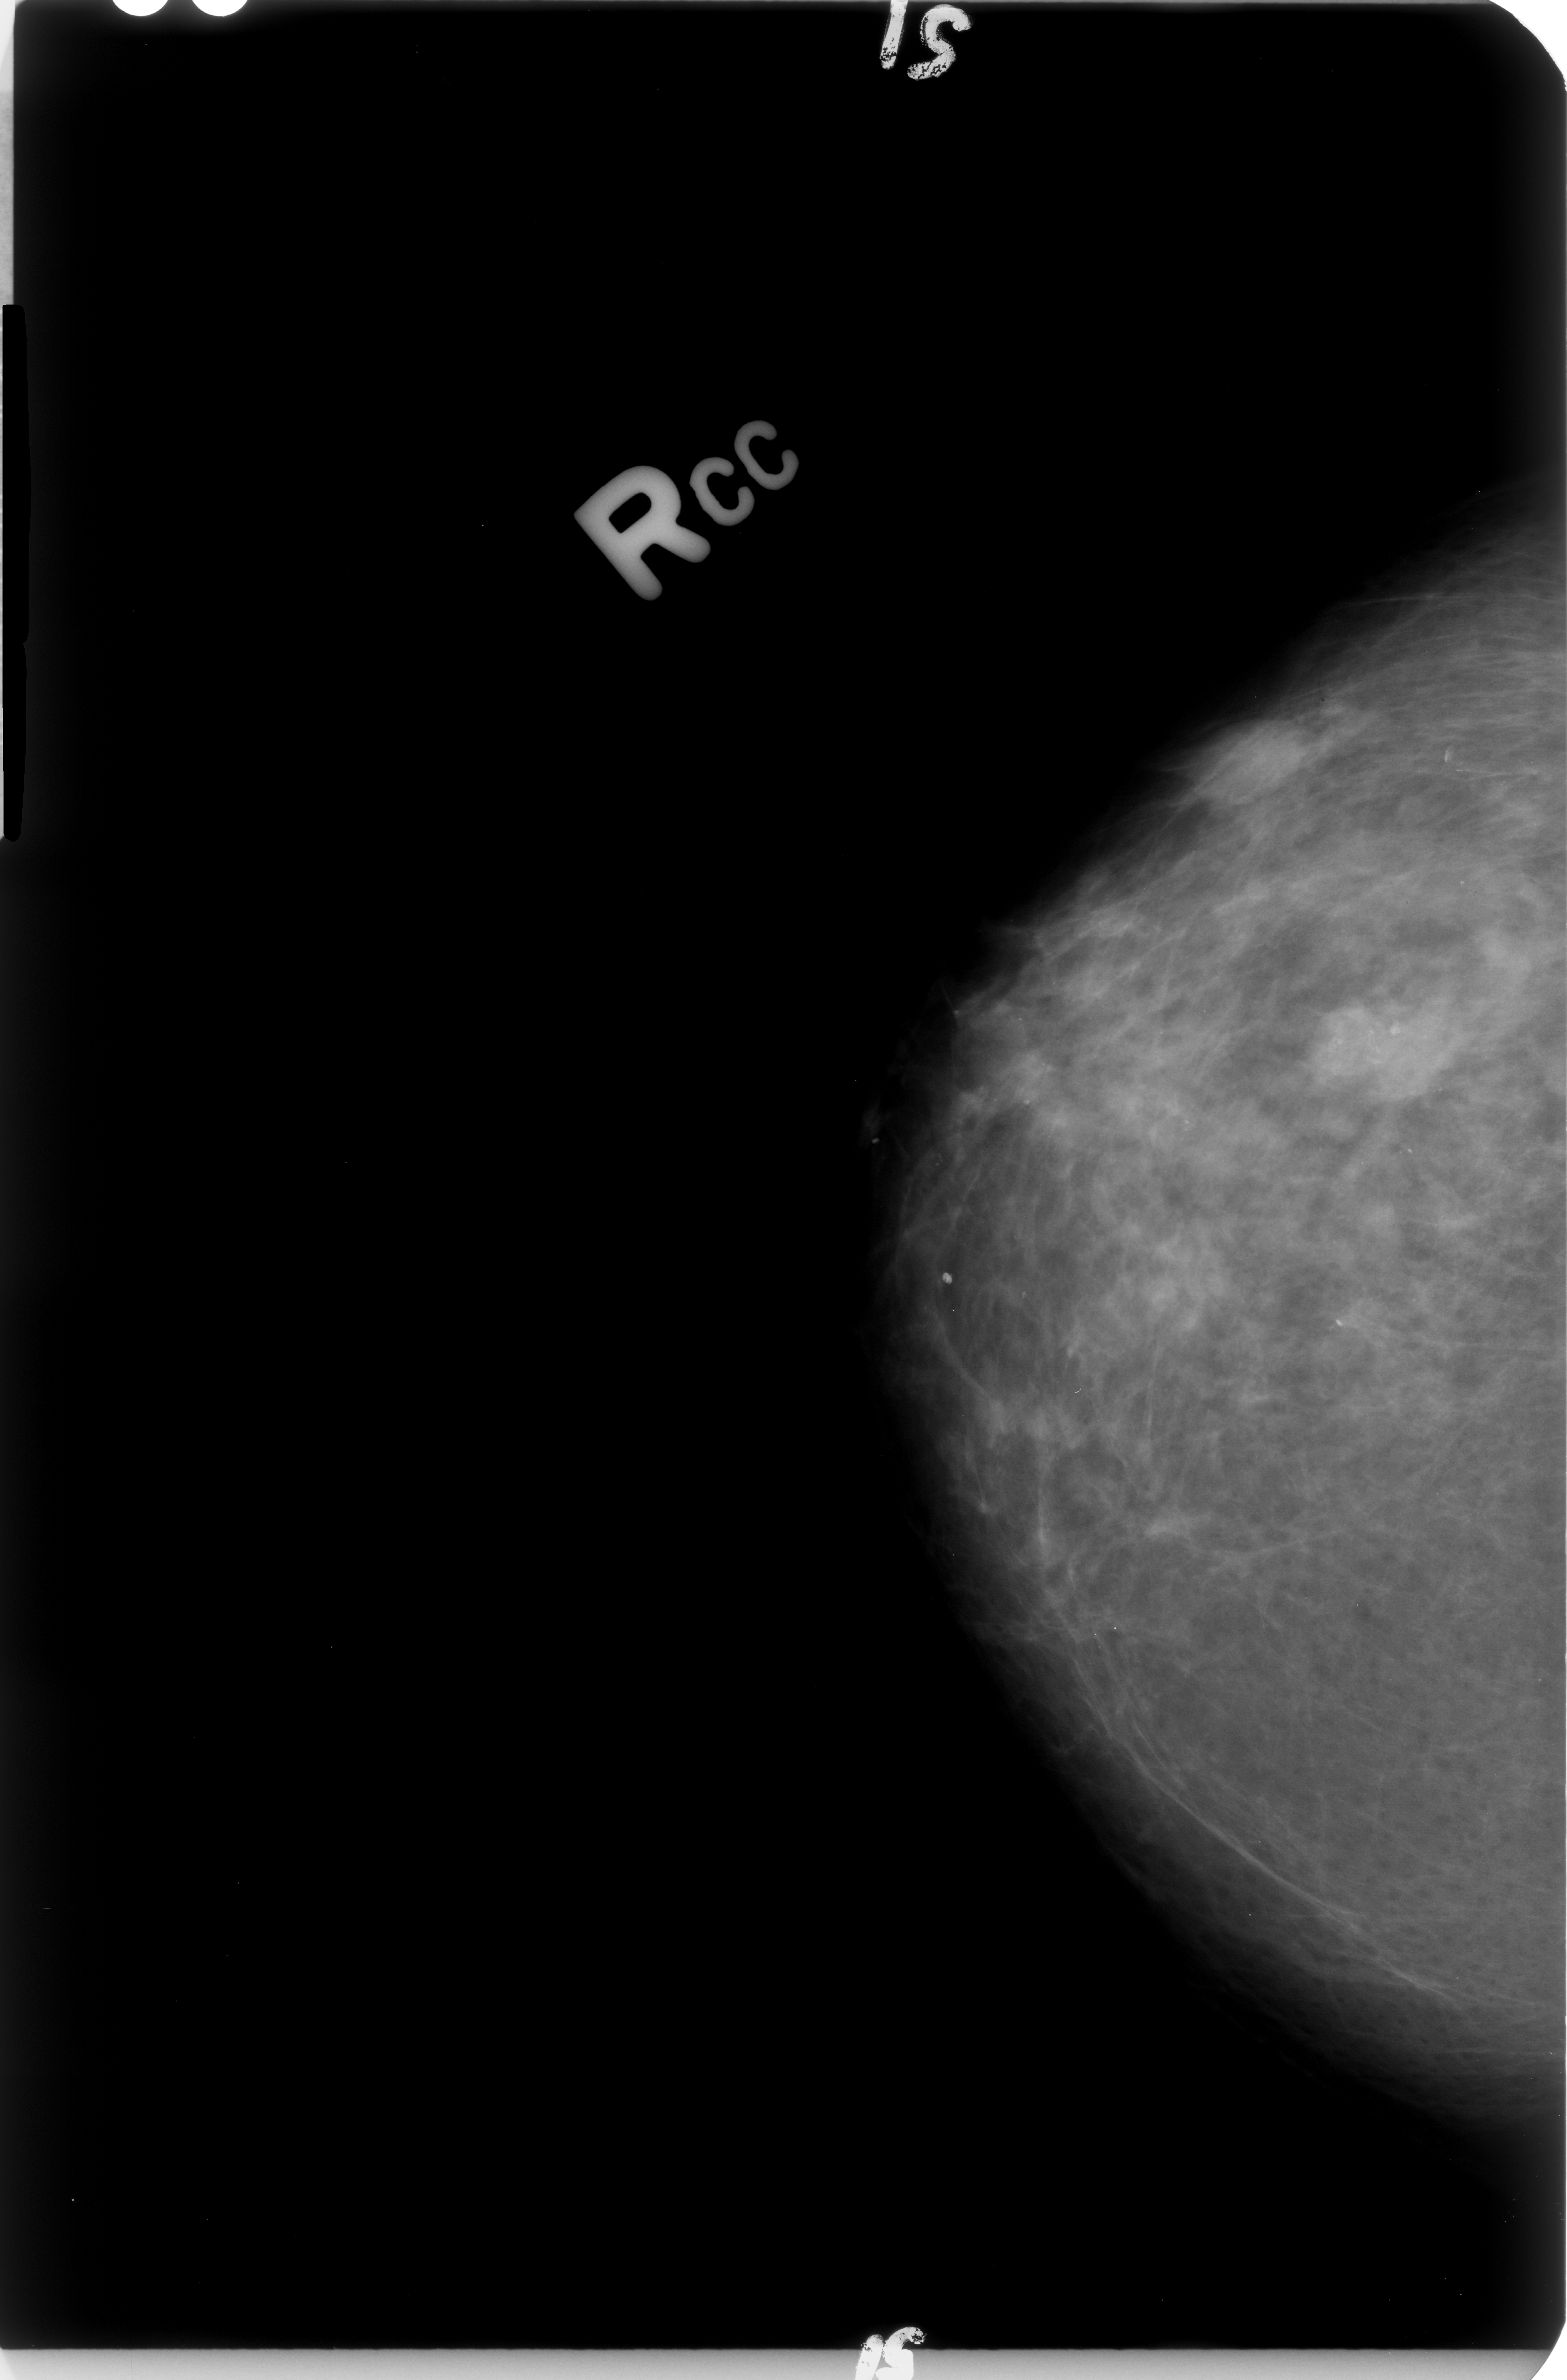
Mammogram (digitized film); right breast; craniocaudal (CC) view; breast composition: scattered fibroglandular densities (BI-RADS density category 2 of 4); 1567 × 2380 image matrix.
Marked abnormalities (boxes around the expert regions of interest):
- calcifications, morphology pleomorphic, distribution clustered; BI-RADS assessment category 4; subtlety rating 3 on a 1 (subtle) to 5 (obvious) scale; pathology result (as recorded, not read from the image): malignant: bounding box (x1, y1, x2, y2) in pixels: (1309, 990, 1471, 1108)